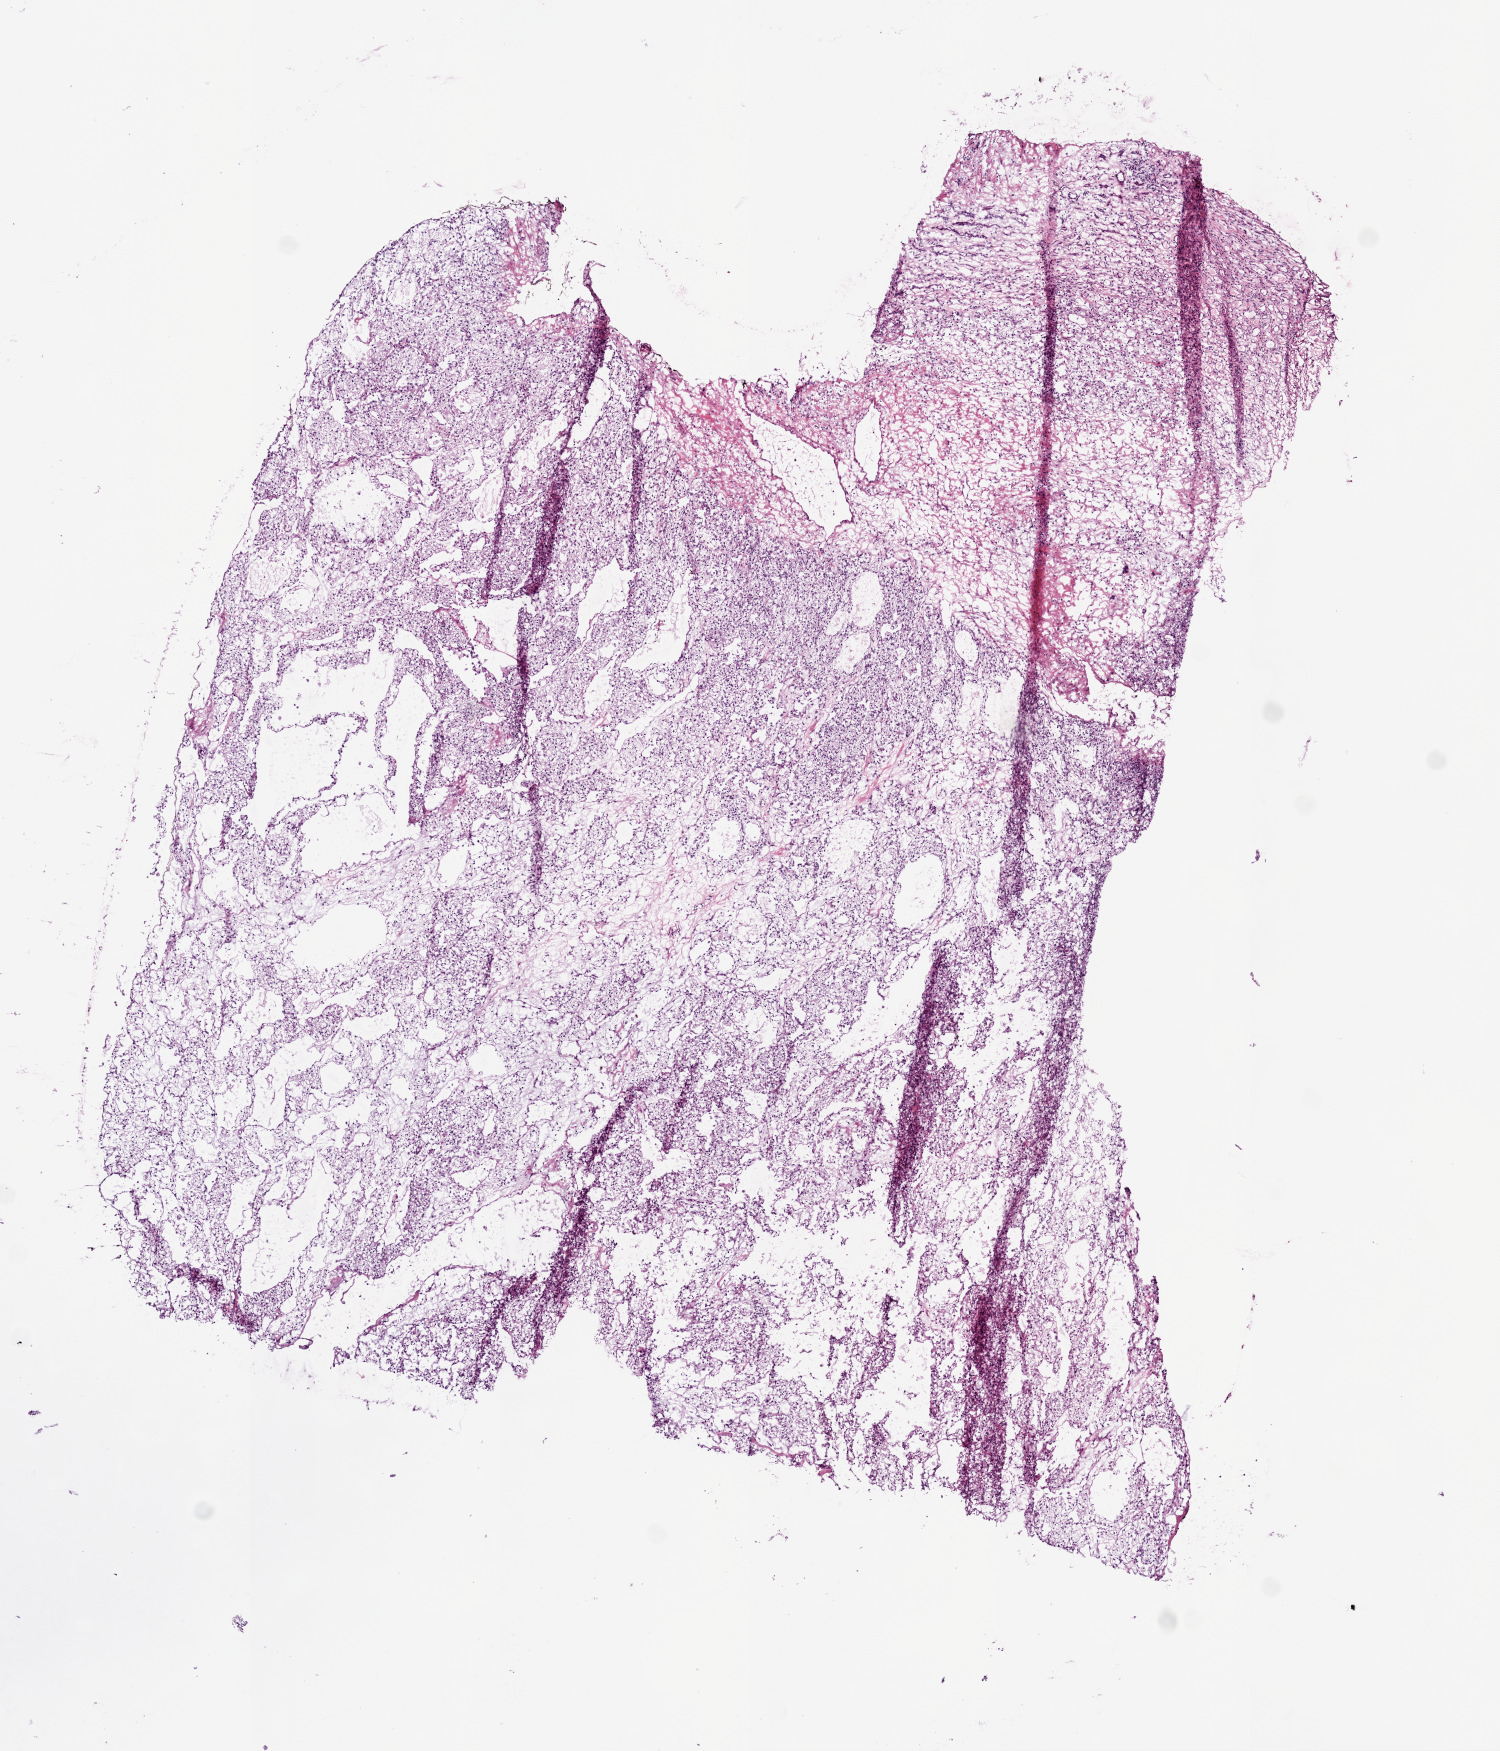
H&E-stained whole-slide image, a low-resolution overview of the entire scanned area, about 6.0 x 7.0 mm, frozen section from the bottom of the tissue portion, sample: primary tumour, kidney. Female, age 54 years at initial diagnosis. Histologic grade: G3 (poorly differentiated). Composition of this section per pathologist review: tumour cells 95%, tumour nuclei 85%, normal cells 0%, stromal cells 5%, necrosis 0%.
* AJCC pathologic stage: I
* TNM: T1b N0 M0
* histologic diagnosis: Clear cell adenocarcinoma, NOS